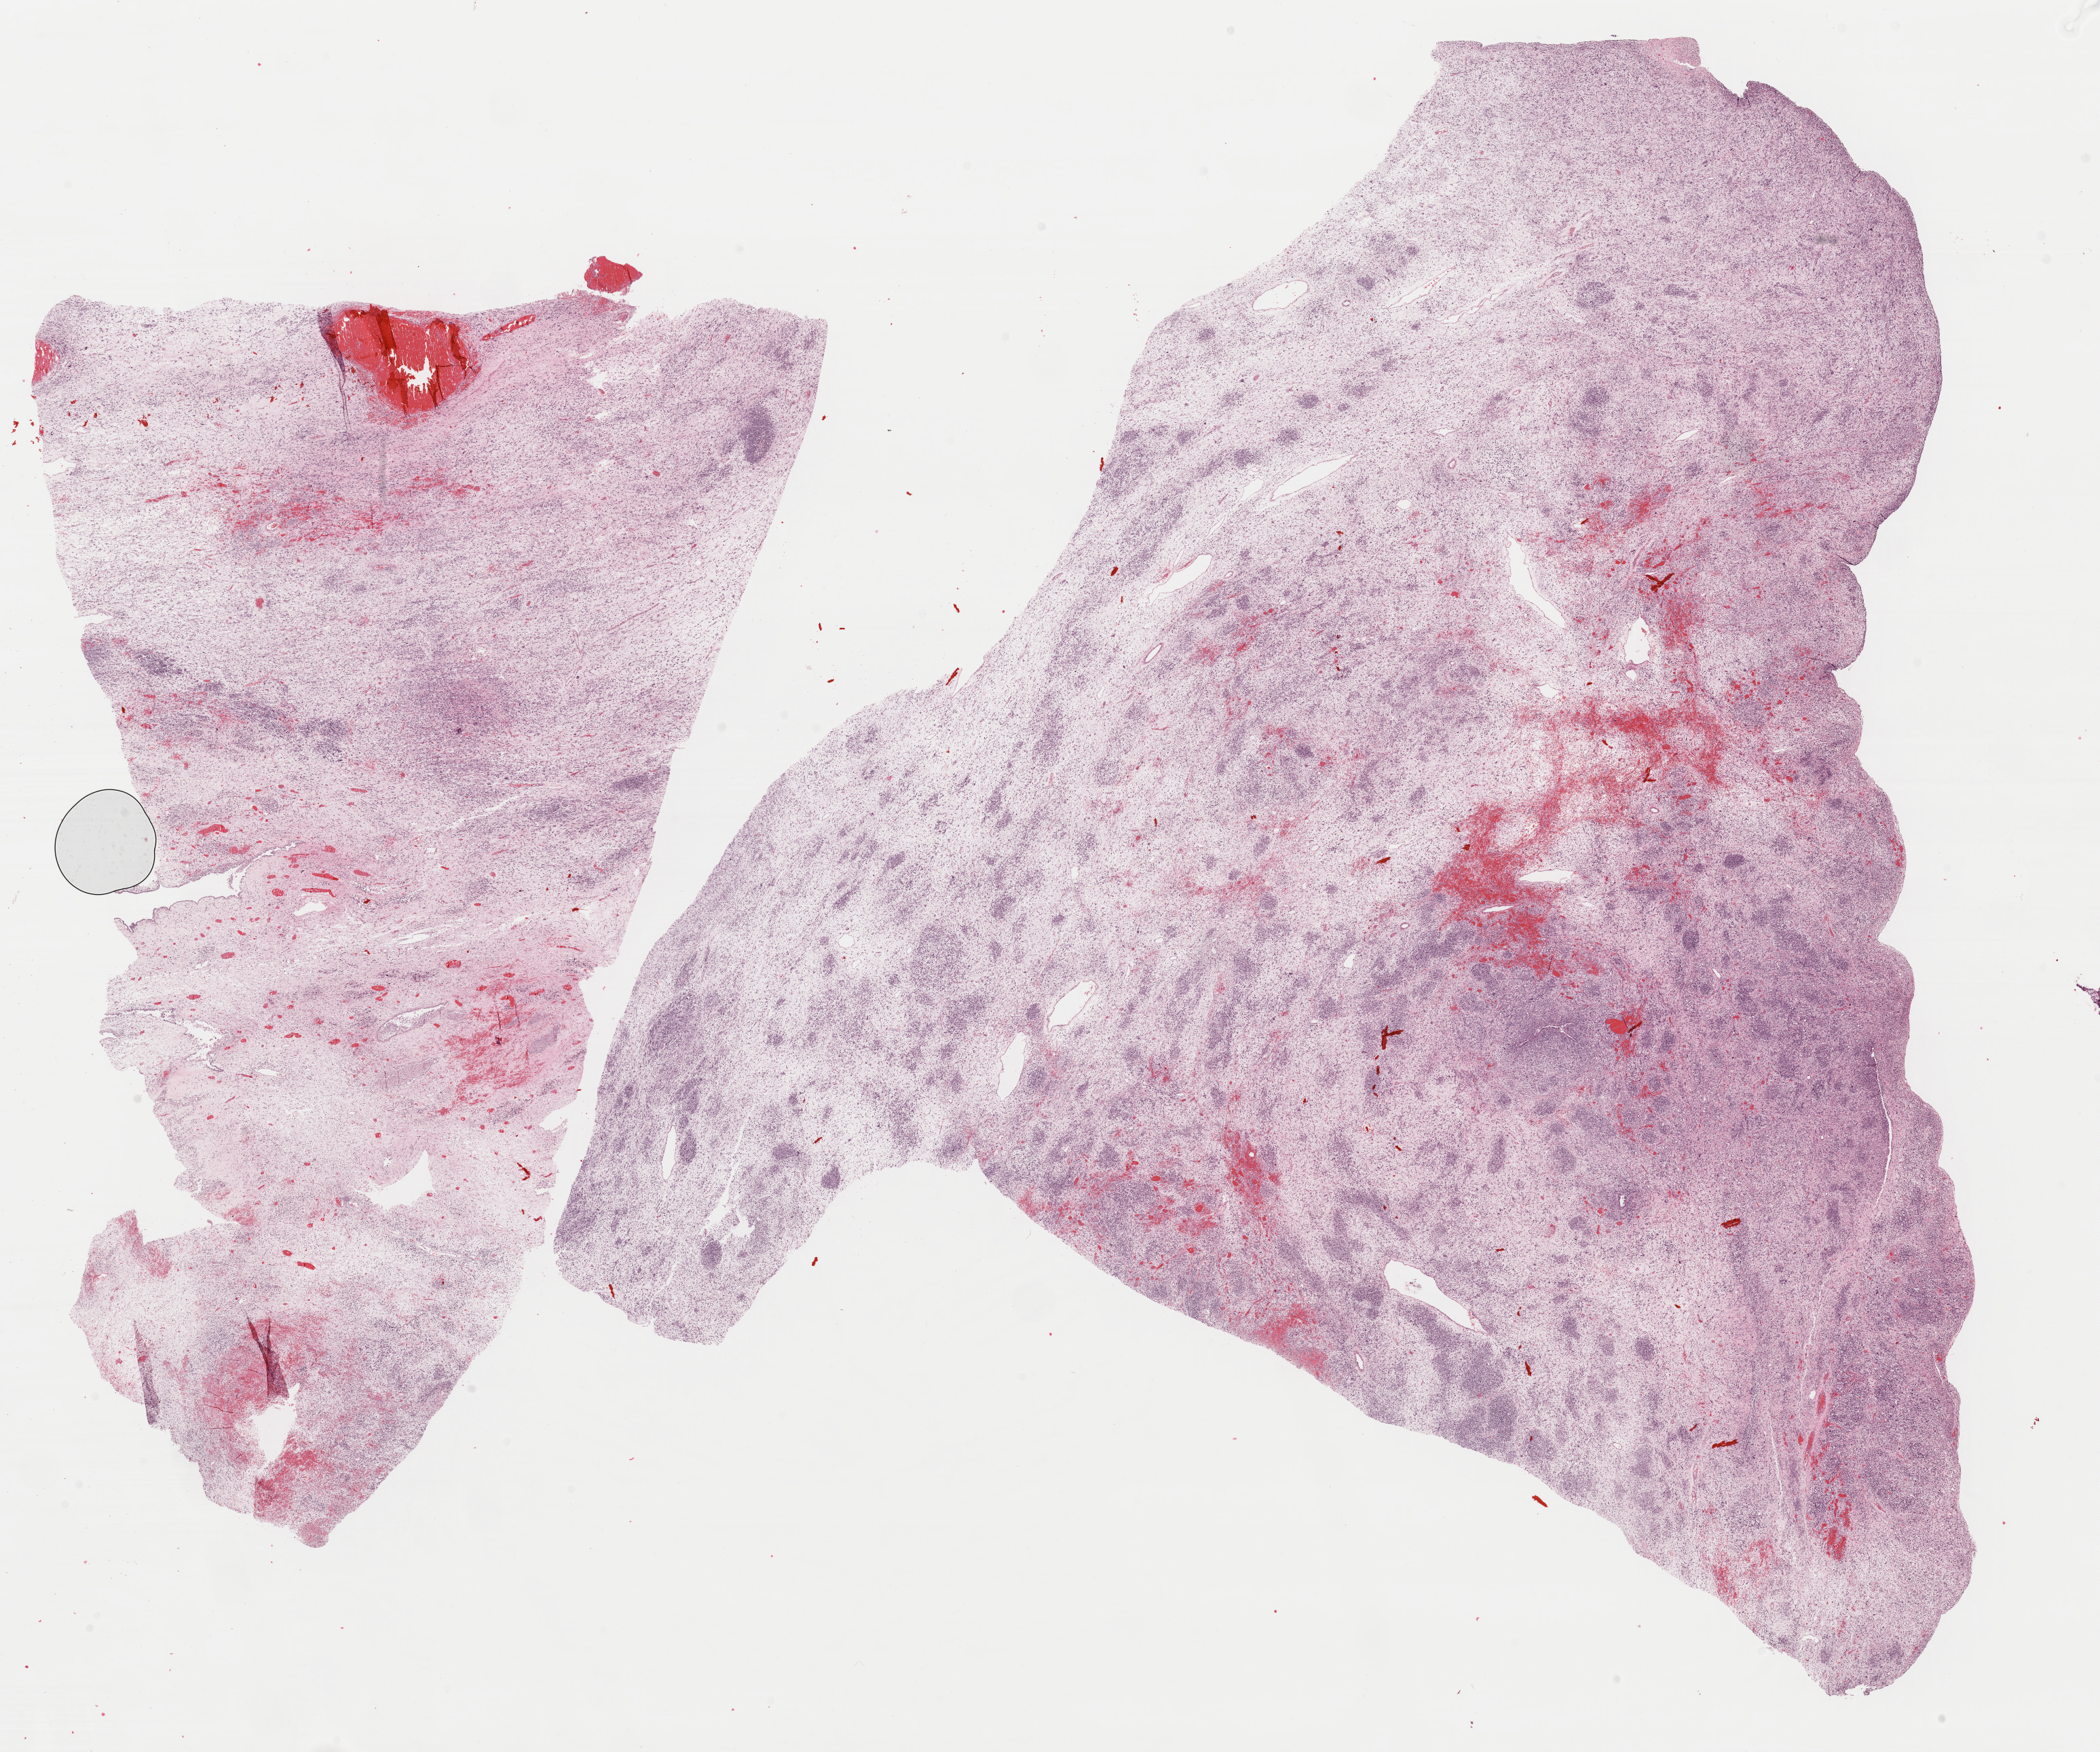
Whole-slide histology image, H&E, a low-resolution overview of the entire scanned area, about 24.4 x 20.4 mm (slide scanned at 40x), FFPE section, sample: primary tumour, uterus. Female patient; age at initial diagnosis 68 years.
FIGO stage: IIIC1. Lymph nodes positive (case pathology): 3 of 20 examined. Pathologic diagnosis: Carcinosarcoma, NOS (endometrium).